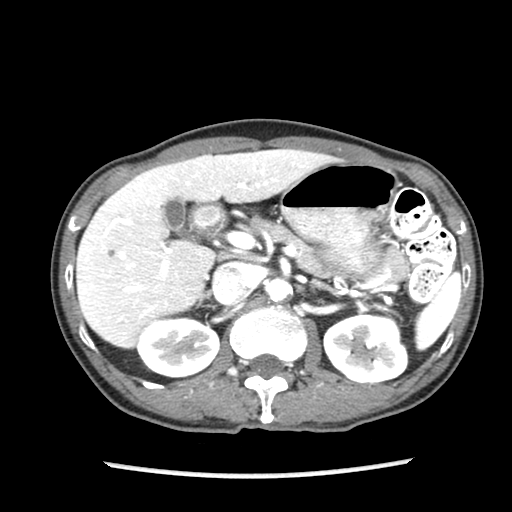
Contrast-enhanced abdominal CT (liver protocol), one axial slice. 140 kVp. Soft-tissue window (W 400 / L 40 HU). 2.5 mm slice thickness. 512 × 512 image matrix. From the clinical record (not read from this slice): diagnosis: hepatocellular carcinoma (patient treated with transarterial chemoembolisation; whether this scan precedes or follows treatment is not stated here); TNM stage (as recorded): Stage-IIIB; Child-Pugh class: A.
Outlined on this slice (semi-automatically segmented with operator editing):
- liver parenchyma outside the tumour (the mass and vessels are separate outlines, so this box may not span the whole liver): bounding box (x1, y1, x2, y2) in pixels: (76, 148, 332, 348)
- liver vessels: (80, 163, 295, 320)